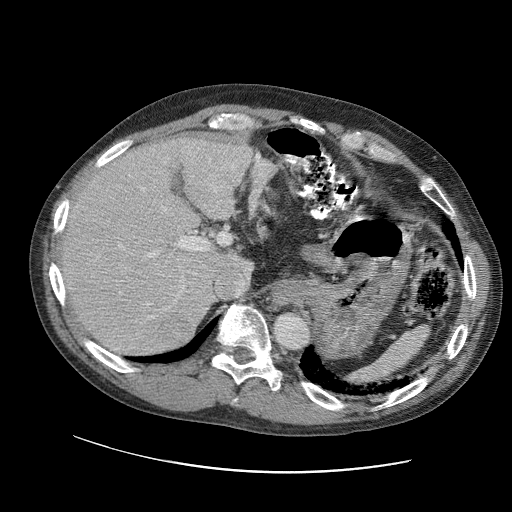
Contrast-enhanced abdominal CT (liver protocol), one axial slice; position 74 of 109 along the scan axis; soft-tissue window (W 400 / L 40 HU); 2.5 mm slice thickness; 512 × 512 image matrix. Case-level facts recorded for this patient, not image findings: diagnosis: hepatocellular carcinoma (patient treated with transarterial chemoembolisation; whether this scan precedes or follows treatment is not stated here); TNM stage (as recorded): Stage-IIIC; Child-Pugh class: B; tumour differentiation: well differentiated; tumour nodularity: uninodular.
Outlined on this slice (semi-automatic segmentation, software-assisted and operator-edited):
- abdominal aorta: bounding box (x1, y1, x2, y2) in pixels: (274, 312, 308, 349)
- liver parenchyma outside the tumour (the mass and vessels are separate outlines, so this box may not span the whole liver): (56, 134, 252, 354)
- mass: (157, 319, 197, 348)
- liver vessels: (86, 154, 250, 320)